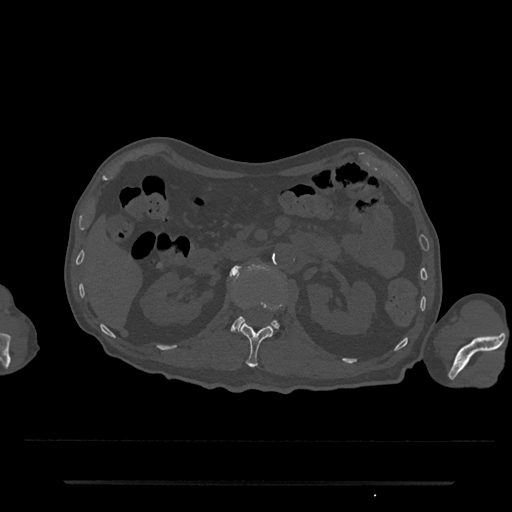
CT including the spine, one axial slice; slice 105 of 797 in the series (ordered by position); bone window (W 1800 / L 400 HU); 0.5 mm slice thickness; 512 × 512 image matrix, field of view 427 × 427 mm. Male patient, age 74 years. Case-level facts recorded for this patient, not image findings: primary cancer: prostate.
Outlined on this slice (semi-automatic segmentation, software-assisted and operator-edited):
- L1 vertebra: bounding box [x1, y1, x2, y2] px = [233, 298, 285, 368]
- L2 vertebra: [230, 265, 279, 331]